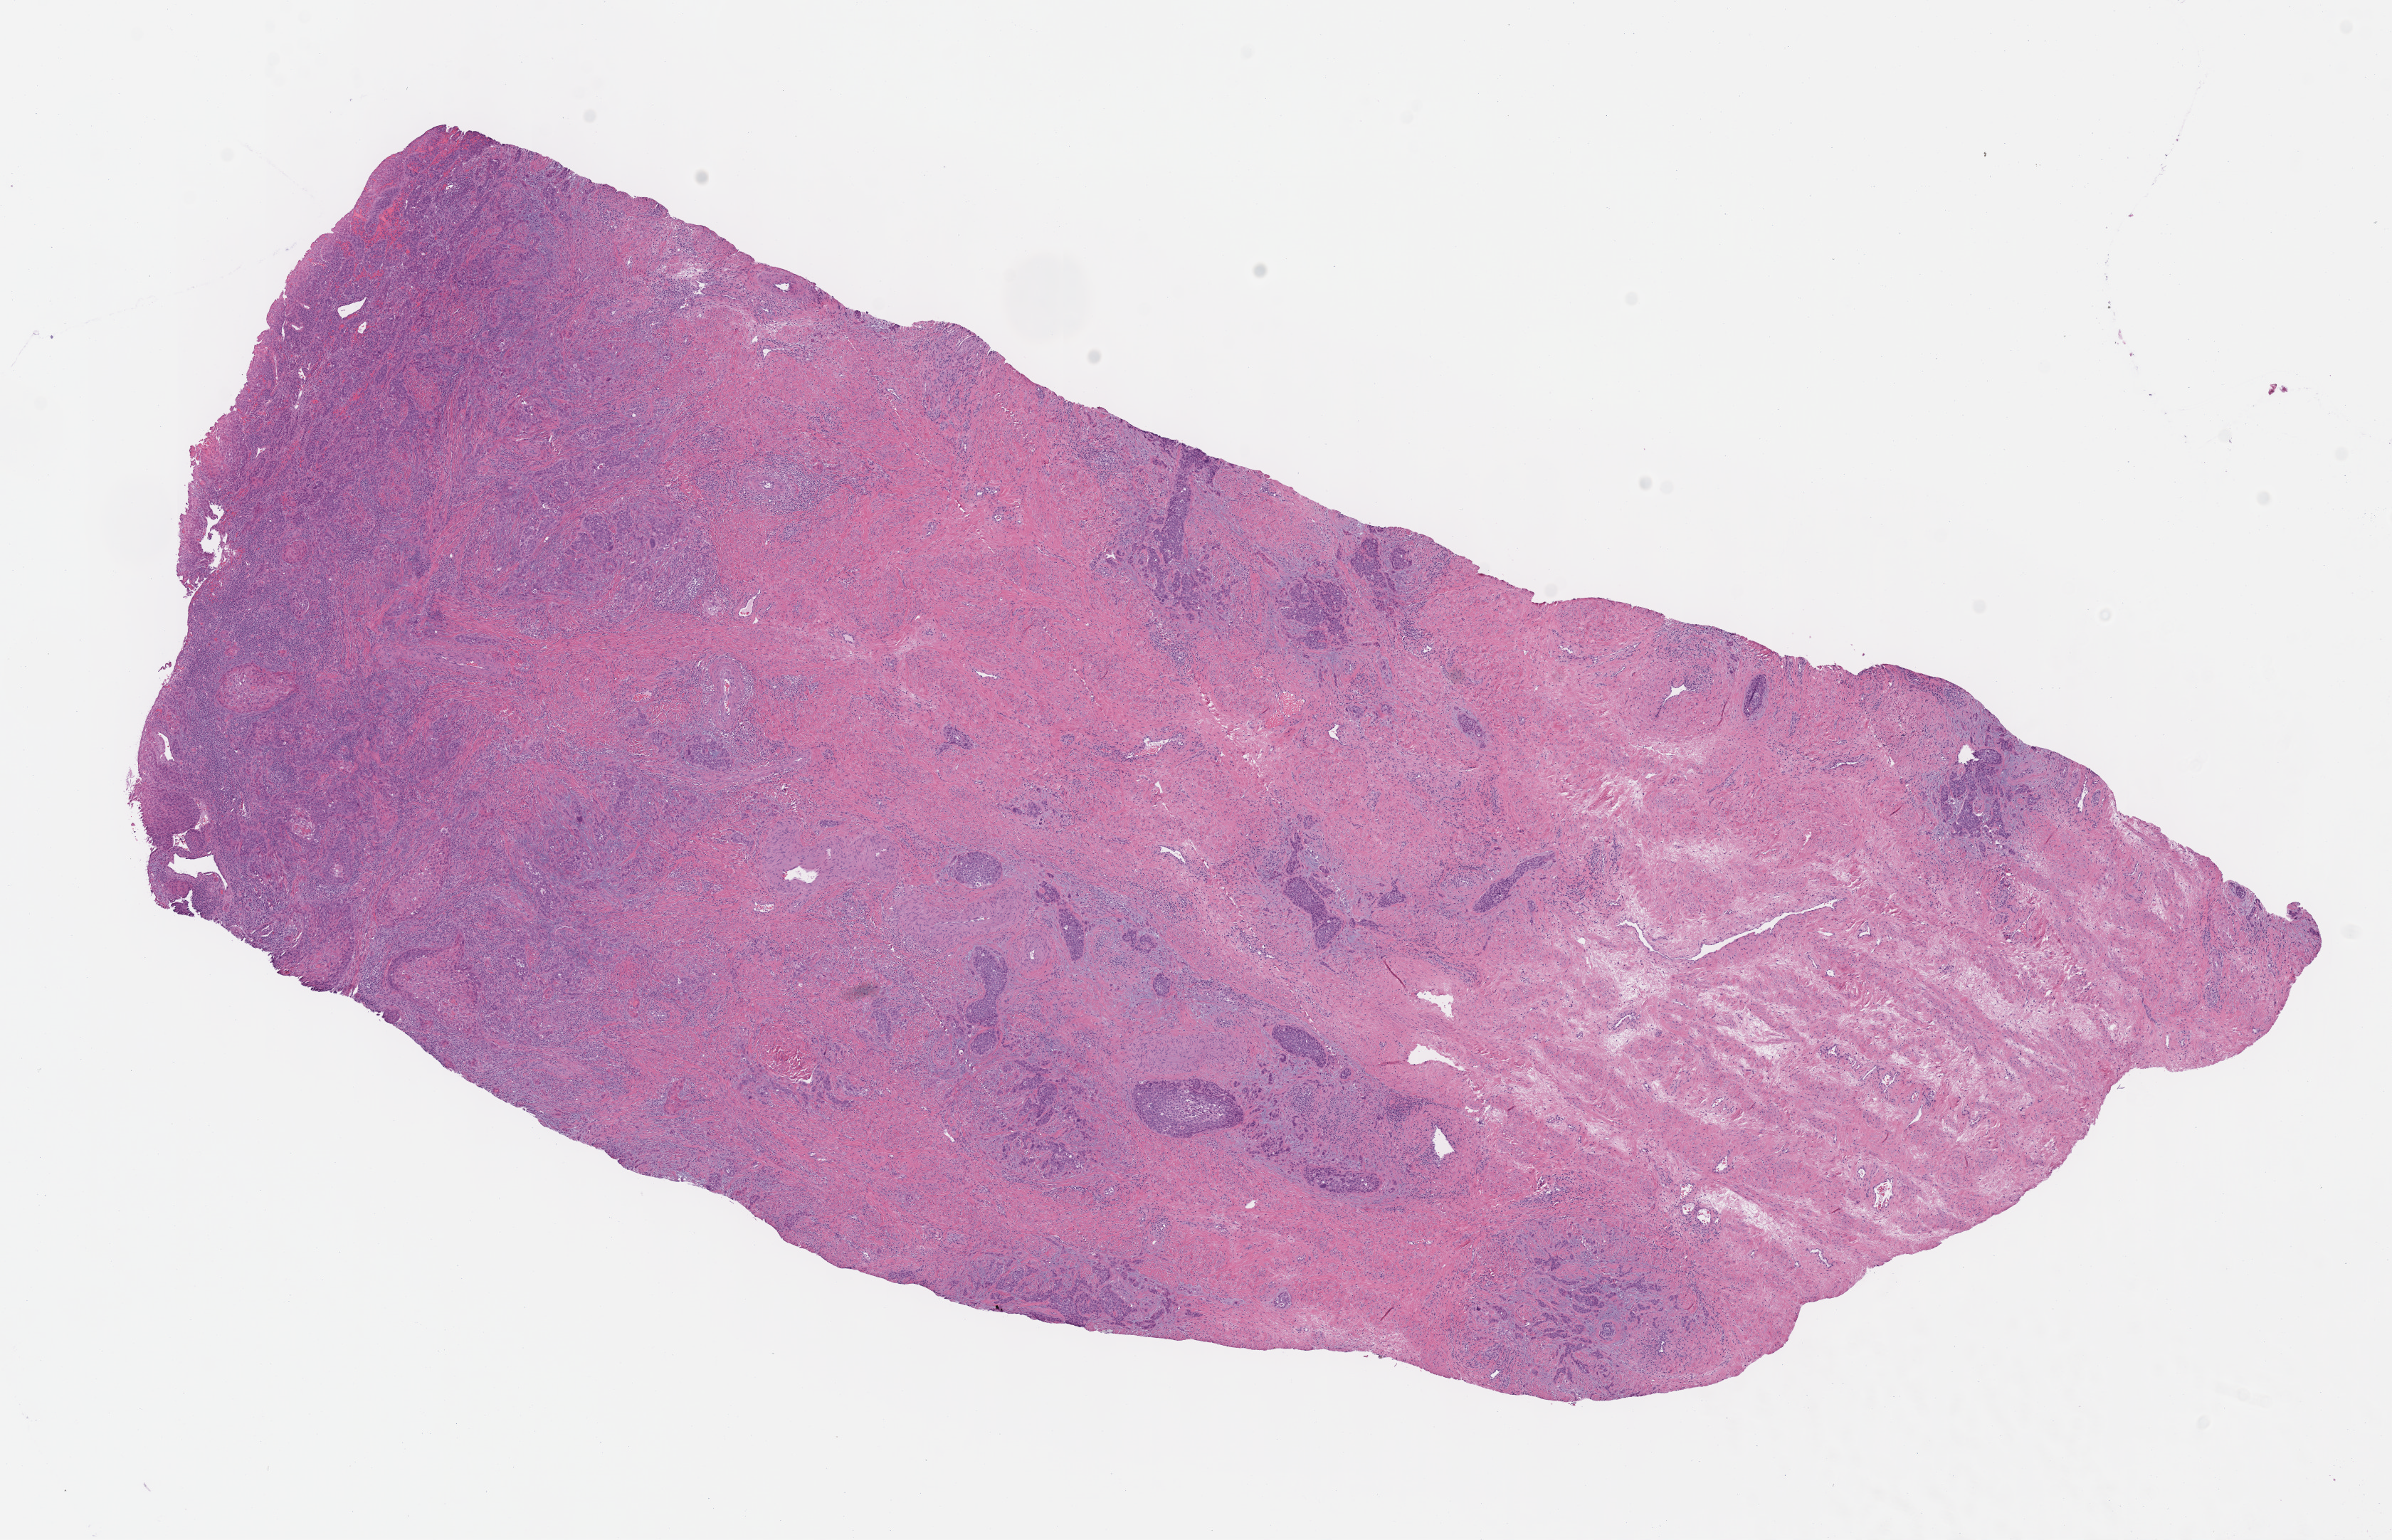
H&E-stained whole-slide image, low-resolution overview of the scanned area, about 13.2 x 8.5 mm; formalin-fixed paraffin-embedded (FFPE) diagnostic section; cervix, primary tumour sample. Female patient; age at initial diagnosis 45 years. Histologic grade: G2 (moderately differentiated).
- pathologic diagnosis: Squamous cell carcinoma, keratinizing, NOS (cervix uteri)
- FIGO stage: IB1